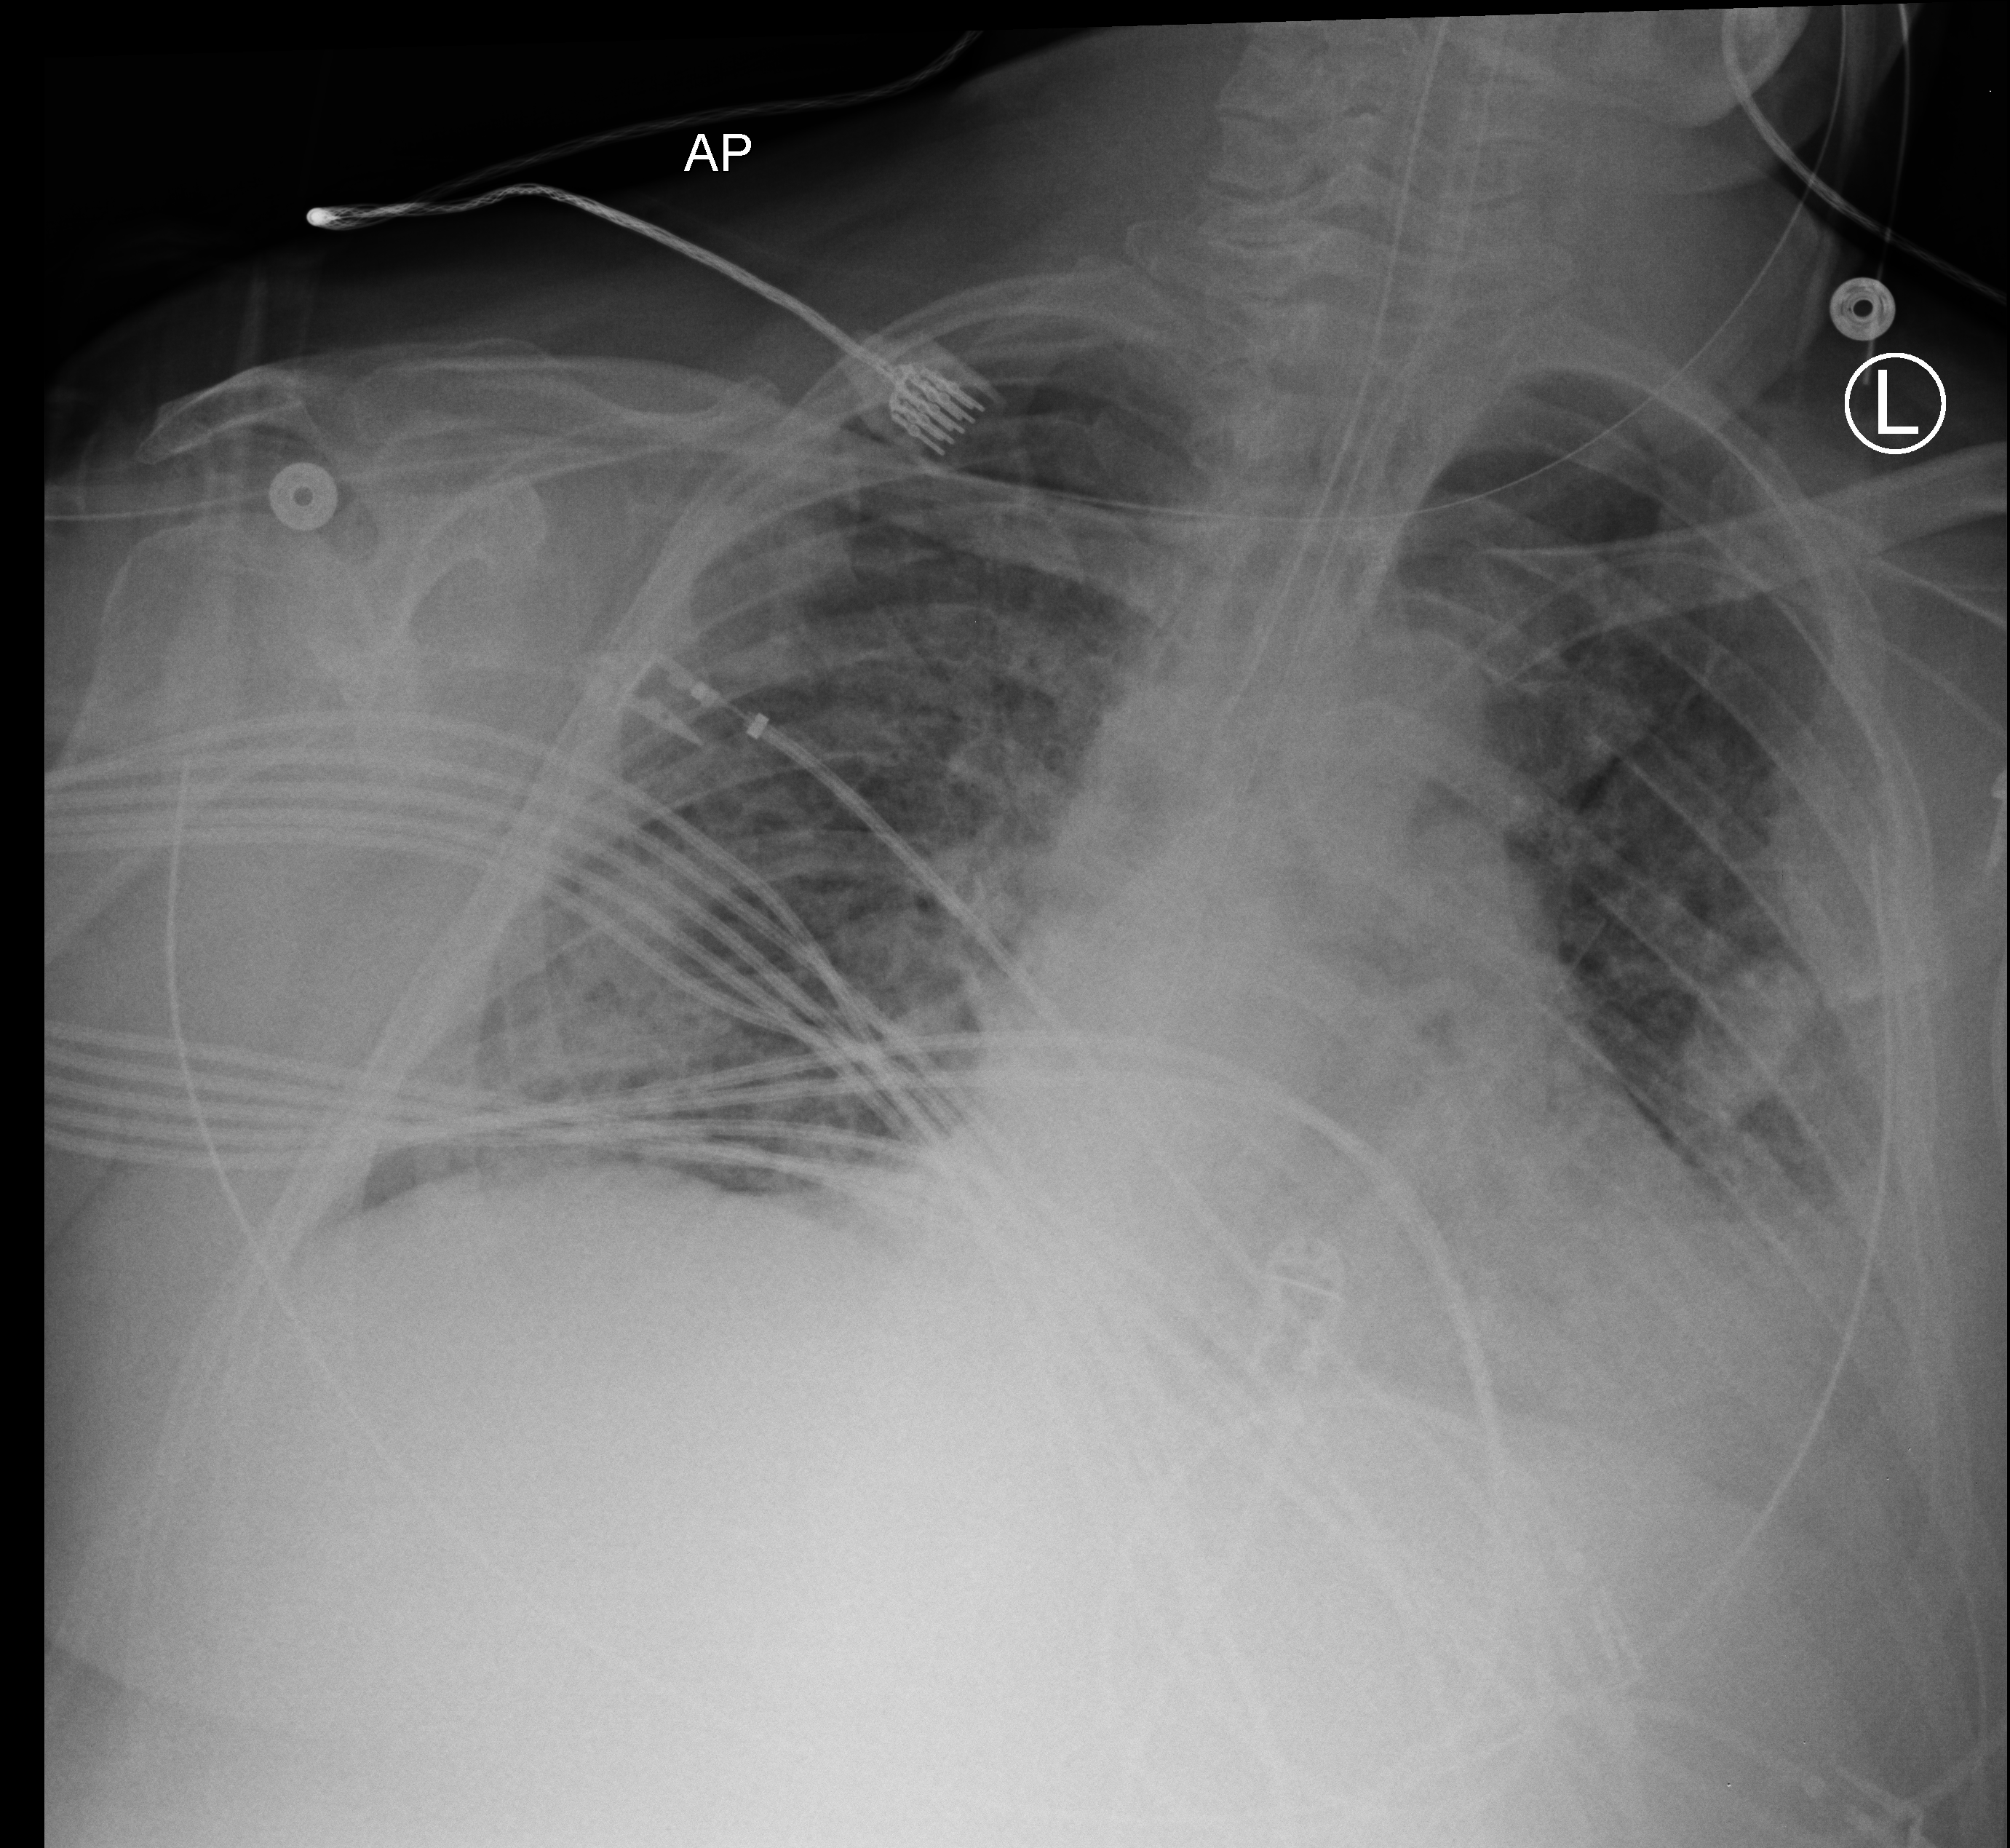
Portable chest radiograph. Patient hospitalised with COVID-19; male, aged 18–59 years.
Hospital-stay facts (about this admission, not read from this image; timing relative to this image not recorded):
- hypertension (admission record): yes
- length of hospital stay: 39 days